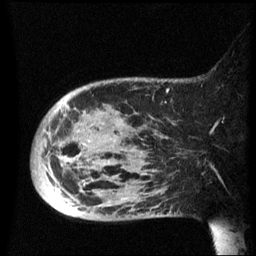
Breast MRI (dynamic contrast-enhanced), one sagittal slice. Slice 15 of 60 in the series (ordered by position). Dynamic contrast-enhanced series, image 2 of 3 at this slice position (ordered by acquisition). 1.5 T. TE 4.2 ms, TR 8.4 ms. 2.5 mm slice thickness. 256 × 256 image matrix, field of view 220 × 220 mm. Patient: female, 49 years.
Structures marked on this image (semi-automatically segmented with operator editing):
- analysis volume of interest (the breast-tissue region the enhancement analysis was run in; not a lesion): bounding box [x1, y1, x2, y2] px = [32, 78, 185, 221]
- tumour enhancement mask (voxels above the 70 % enhancement threshold inside the analysis volume of interest): [49, 106, 71, 185]